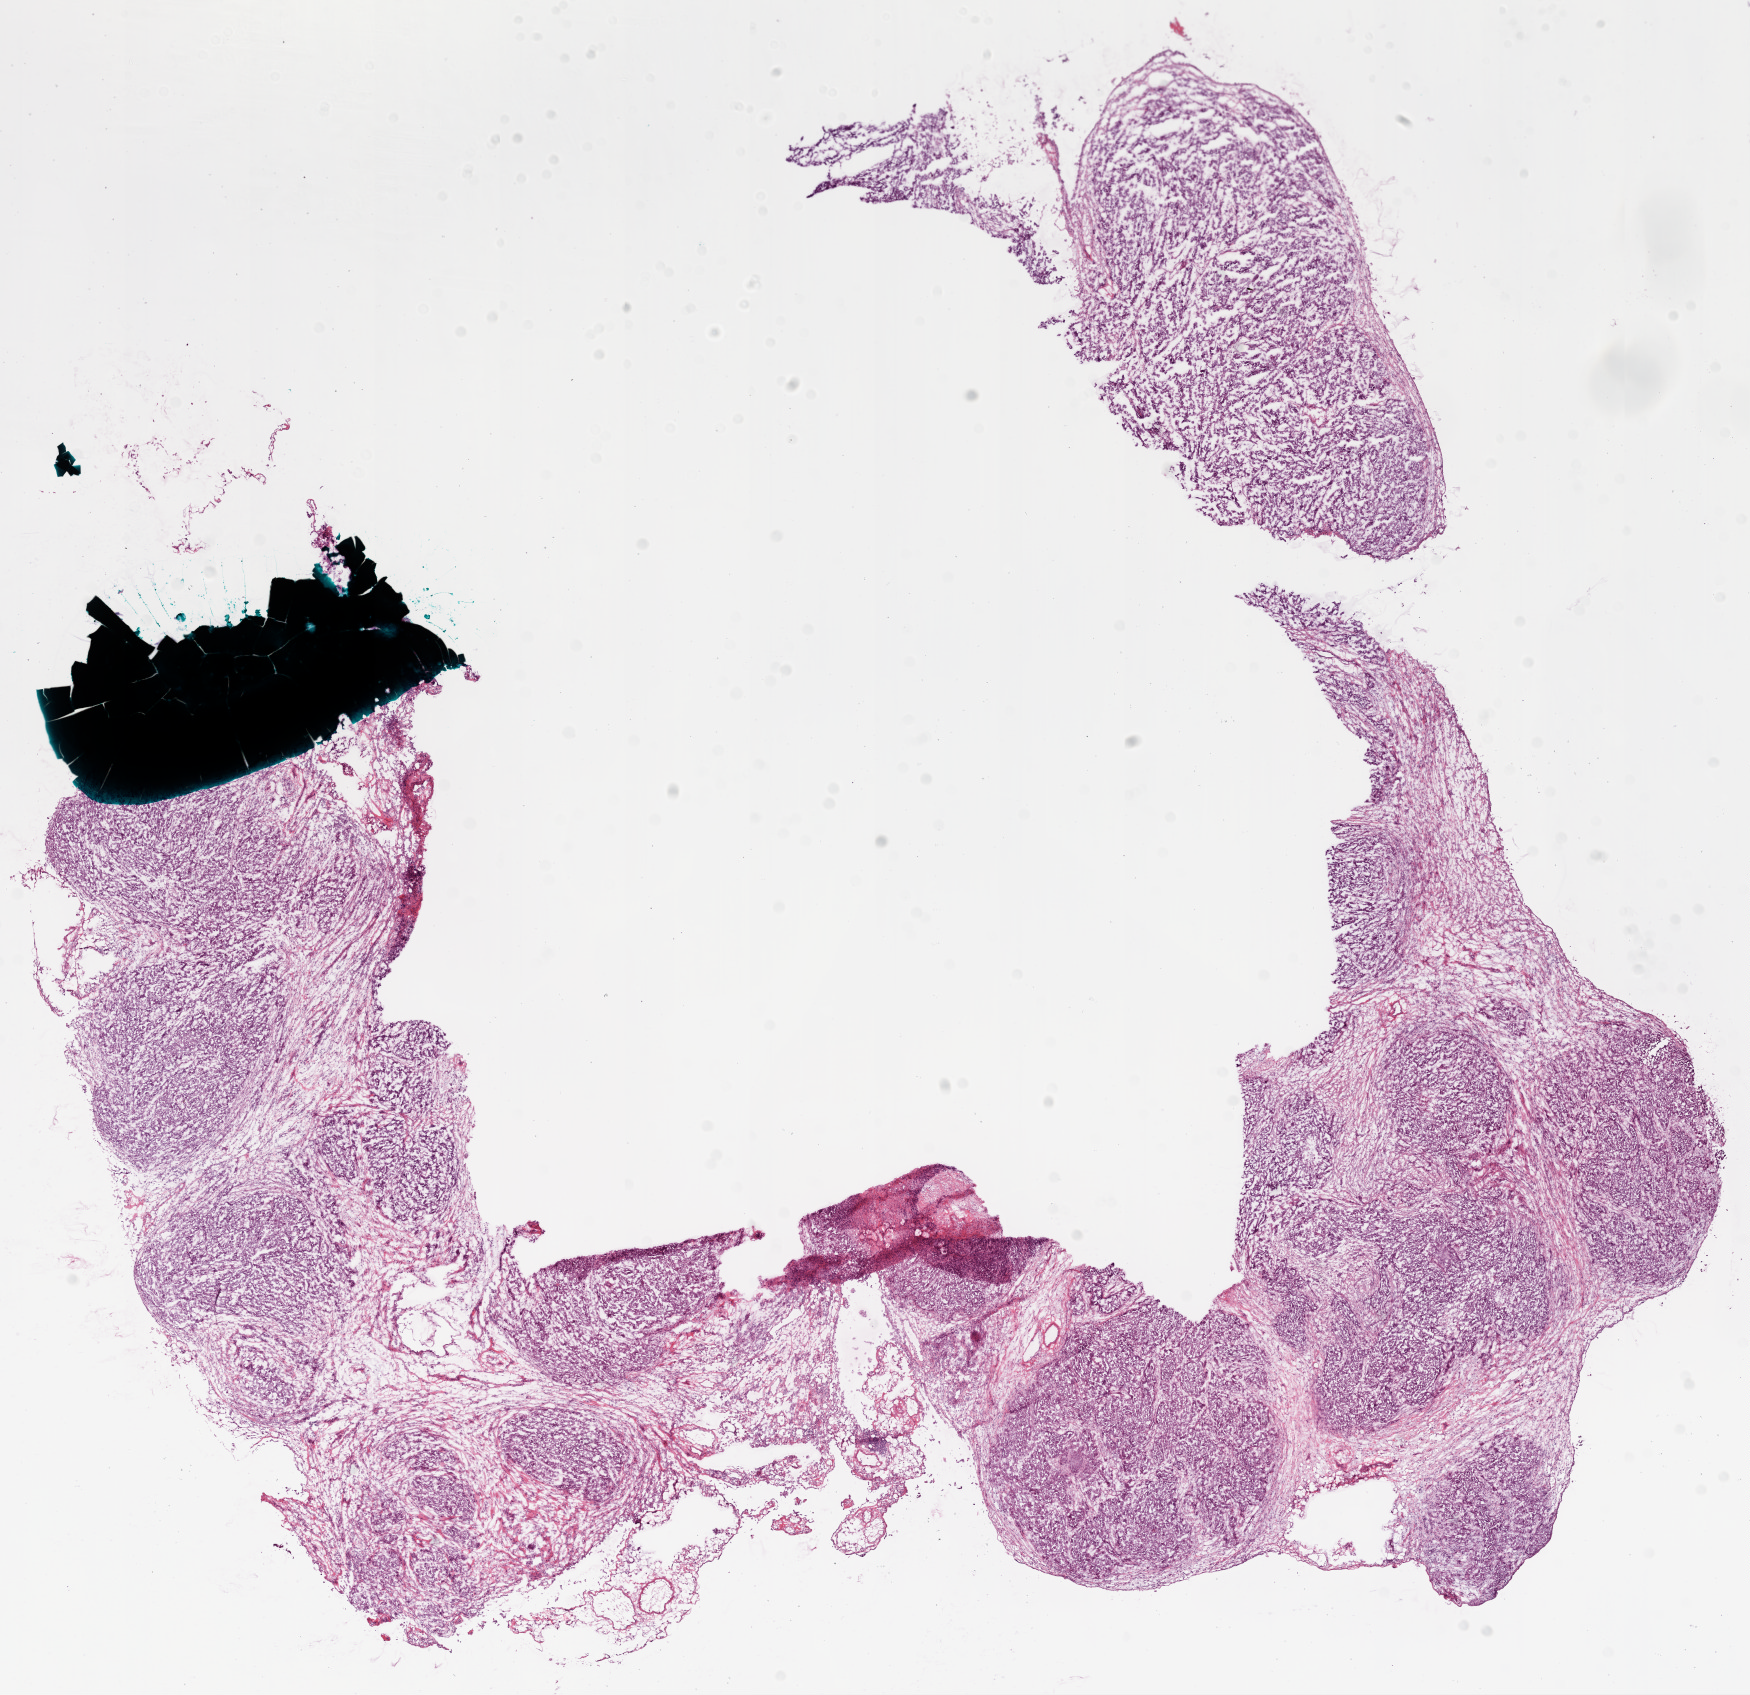
Whole-slide histology image, H&E-stained — shown as a low-resolution overview of the whole scanned area (about 14.0 x 13.6 mm); frozen section from the bottom of the tissue portion; primary tumour sample from the ovary. Patient: female, age at initial diagnosis 58 years. Histologic grade: G3 (poorly differentiated). Composition of this section per pathologist review: tumour cells 90%, tumour nuclei 90%, normal cells 0%, stromal cells 10%, necrosis 0%.
• diagnosis: Serous cystadenocarcinoma, NOS
• FIGO stage: IV